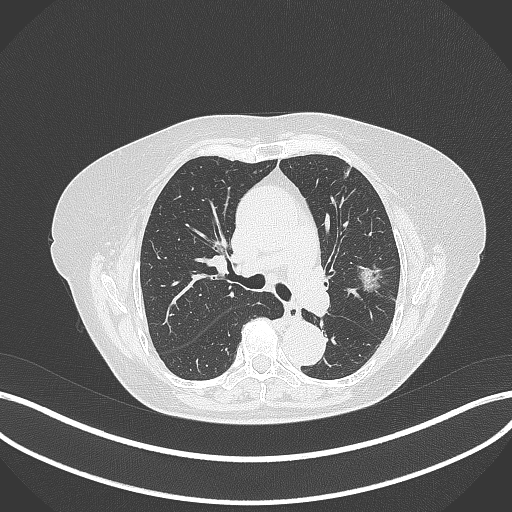
Chest CT, one axial slice; position 206 of 316 along the scan axis; reconstruction kernel B70f; lung window (W 1500 / L -600 HU); 1 mm slice thickness; 512 × 512 image matrix. Patient: female, 75 years. Case-level facts recorded for this patient, not image findings: clinical TNM (as recorded): T1c N0 M0.
Annotated regions visible in this slice (rectangle marked by the reading radiologist):
- lung tumour (recorded histology: adenocarcinoma): bounding box <352,263,387,300> (left, top, right, bottom; pixels)